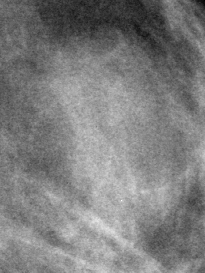
Crop from a digitized film mammogram around one marked abnormality, left breast, MLO view.
Marked abnormality: mass, shape lobulated, margins circumscribed; BI-RADS assessment category 3; subtlety rating 4 on a 1 (subtle) to 5 (obvious) scale; pathology (as recorded): benign.